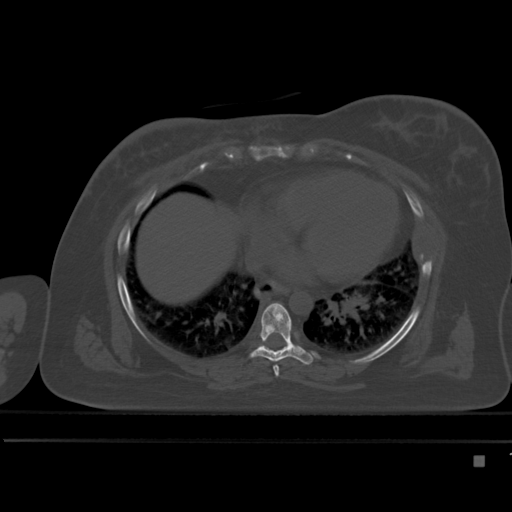
CT including the spine, one axial slice. Bone window (W 1800 / L 400 HU). 512 × 512 image matrix, field of view 404 × 404 mm. Patient: female, 33 years. From the clinical record (not read from this slice): primary cancer: breast; vertebrae with lytic lesions (as recorded): T1.
Outlined on this slice (semi-automatically segmented with operator editing):
- T6 vertebra: bounding box [x1, y1, x2, y2] px = [273, 365, 280, 377]
- T7 vertebra: [250, 303, 313, 365]